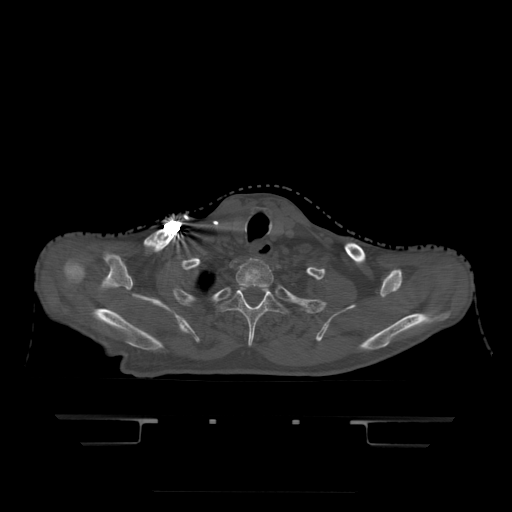
CT including the spine, one axial slice. Slice 390 of 522 in the series (ordered by position). Bone window (W 1800 / L 400 HU). 1.25 mm slice thickness. 512 × 512 image matrix. Patient age 68 years. From the clinical record (not read from this slice): primary cancer: urothelial.
Outlined on this slice (semi-automatically segmented with operator editing):
- T1 vertebra: bounding box [x1, y1, x2, y2] px = [236, 259, 274, 289]
- T2 vertebra: [219, 286, 289, 348]